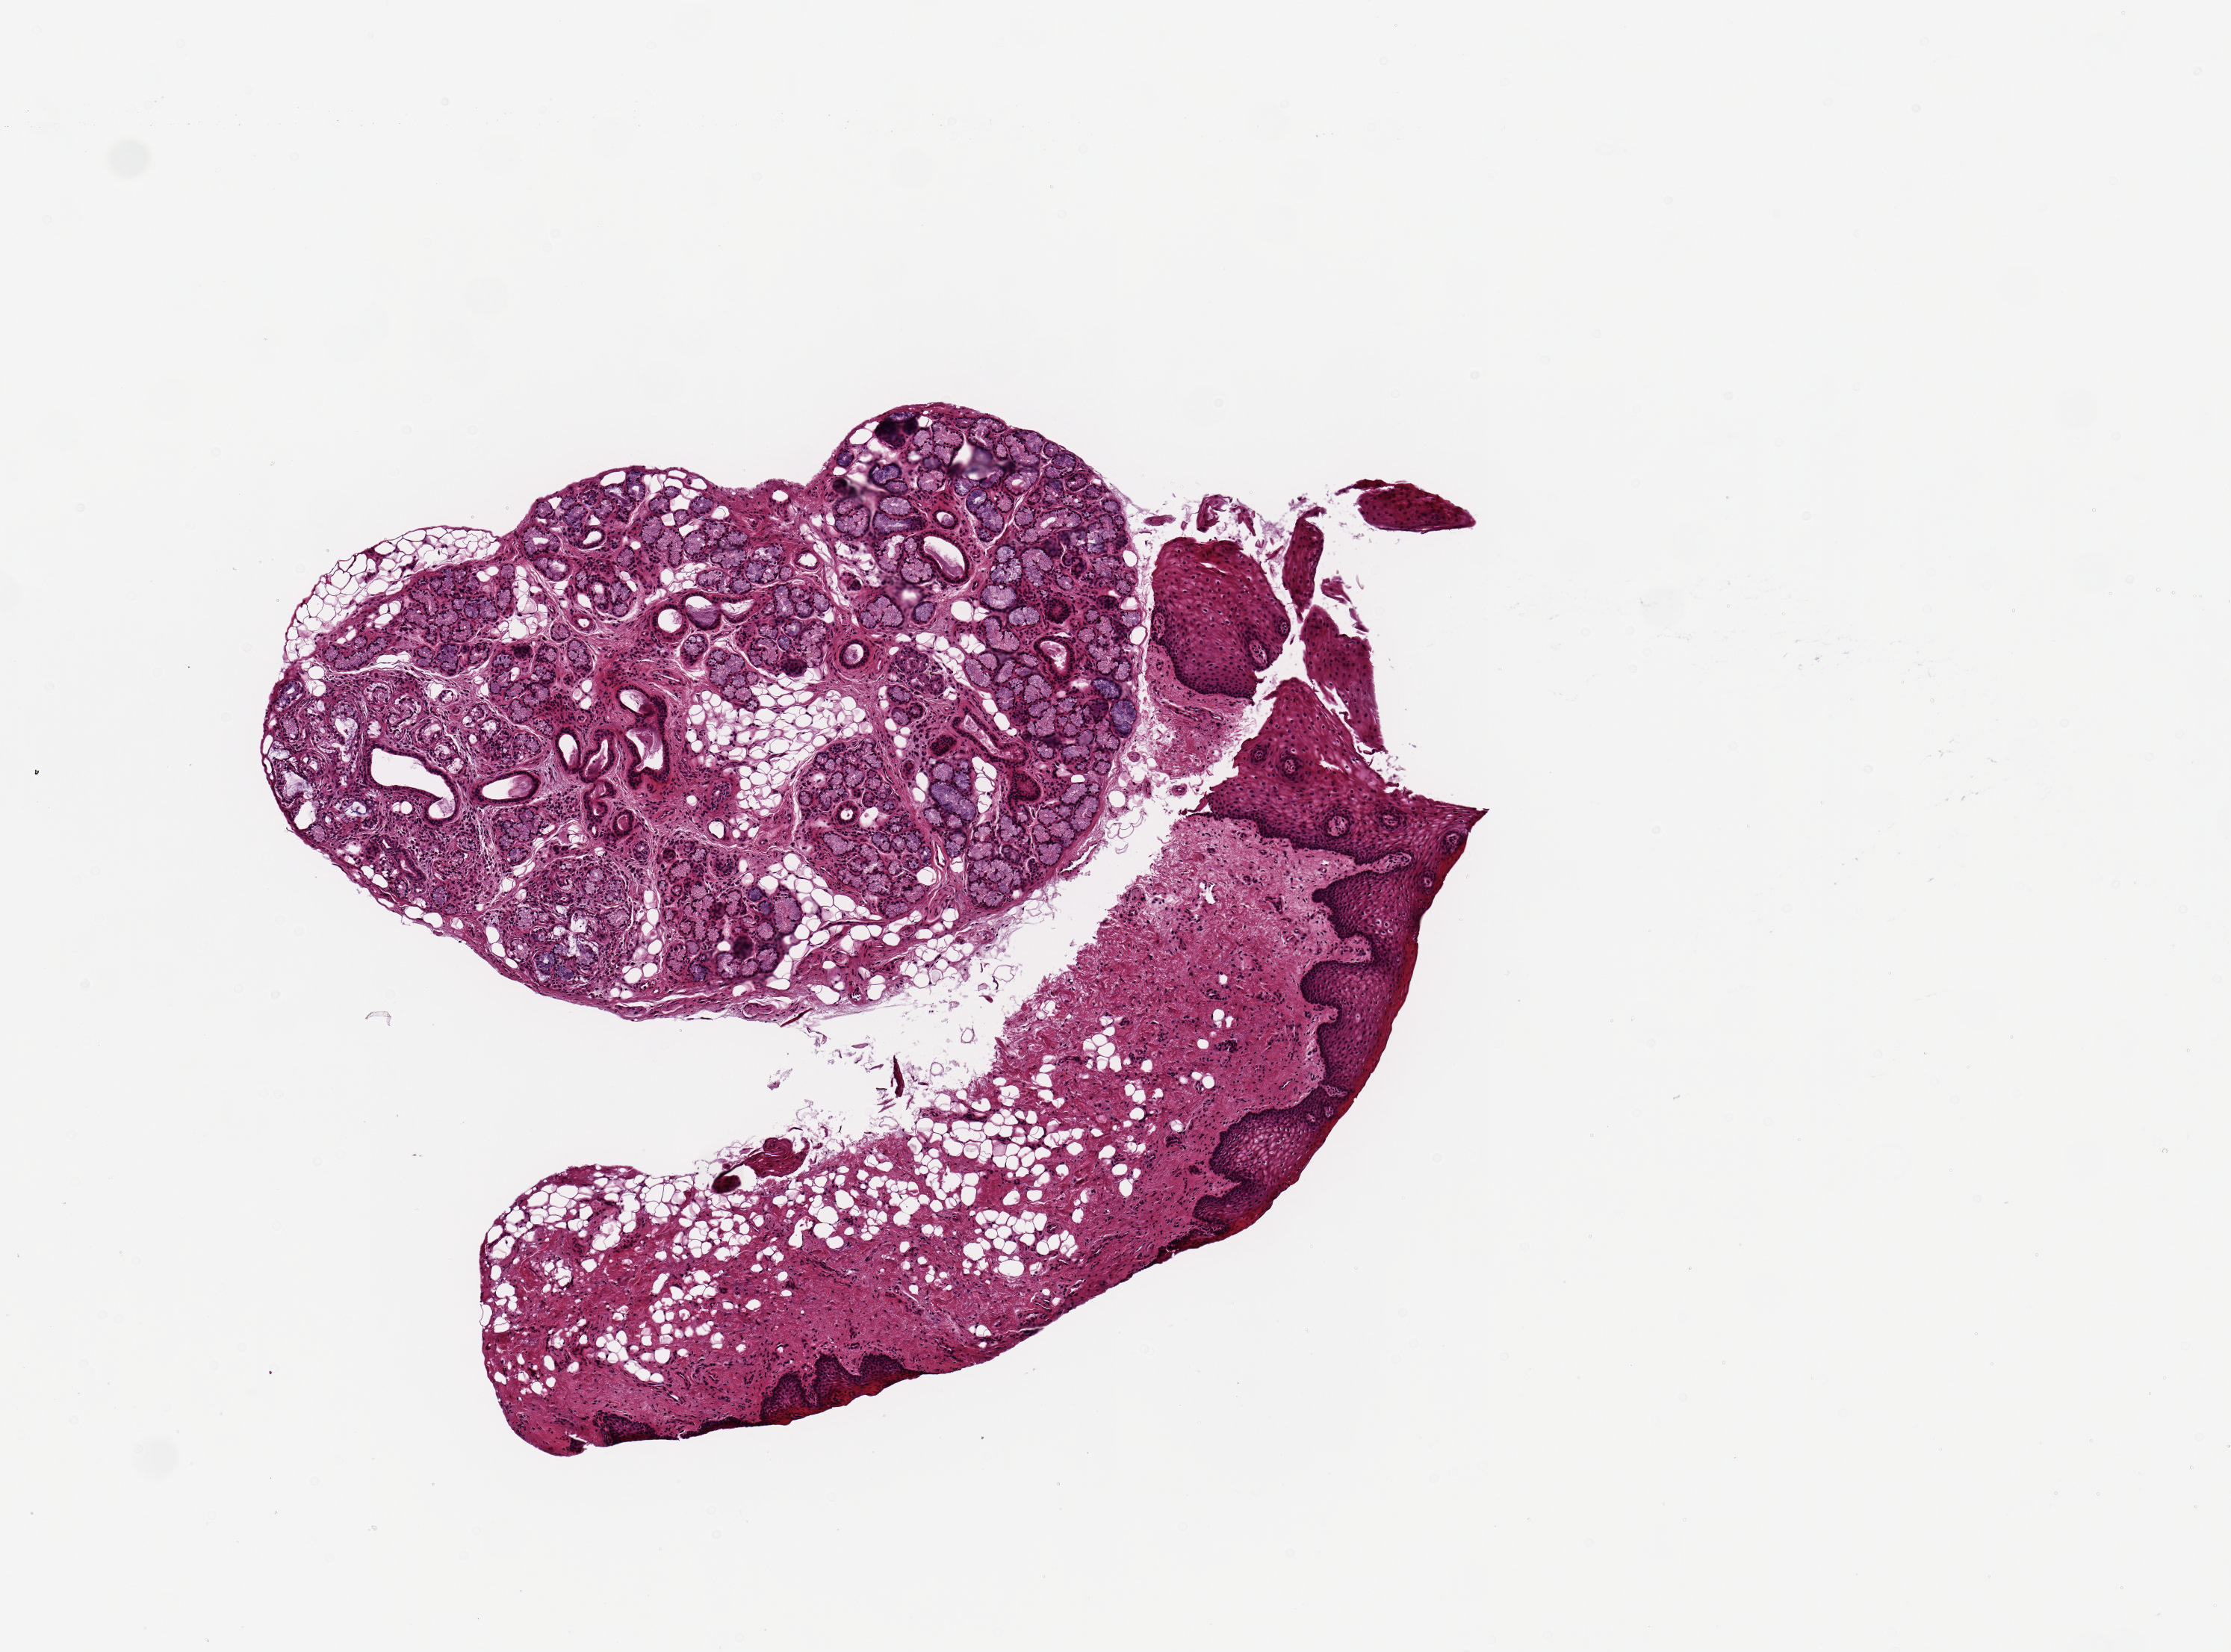
Digitized haematoxylin and eosin-stained section — whole scanned area (about 5.9 x 4.4 mm, slide scanned at 20x) shown as a low-resolution overview. PAXgene-fixed, paraffin-embedded tissue. Section of minor salivary gland (target tissue). Donor tissue sample.
Reviewer comment on this tissue sample: 1 piece, 3x2.5mm; actual glandular tissue is ~2.5x1.5mm; rest is aderhent sqaumous mucosa/stromal tissue.